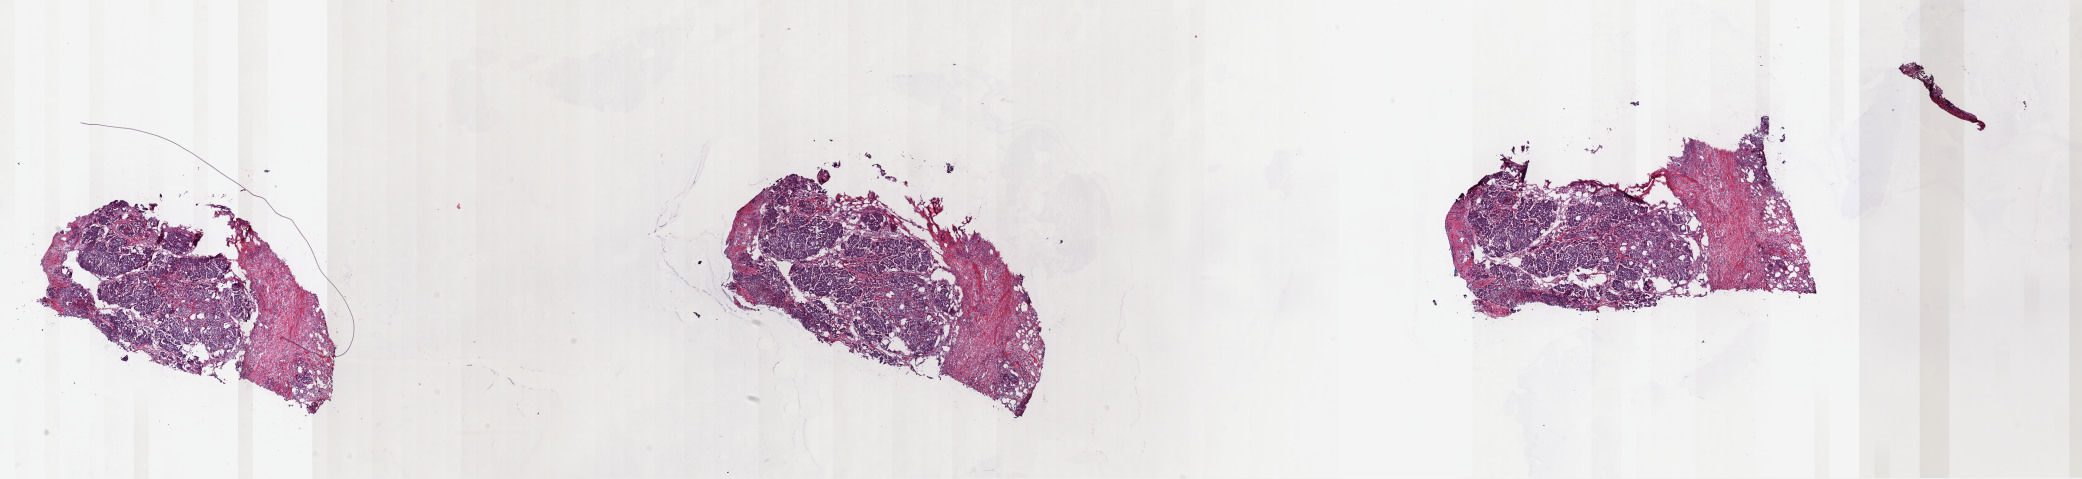
Digitized Hematoxylin and eosin (H&E) stained tissue section (whole slide) — shown as a low-resolution overview of the whole scanned area (about 32.9 x 7.6 mm, acquisition: 40x scan), frozen section from the top of the tissue portion, bladder, primary tumour sample. Male, age 65 years at initial diagnosis. Histologic grade: high grade. Composition of this section per pathologist review: tumour cells 55%, tumour nuclei 65%, normal cells 40%, stromal cells 0%, necrosis 5%. Inflammatory infiltration, as recorded: lymphocyte infiltration 10%, monocyte infiltration 1%, neutrophil infiltration 1%.
Diagnosis: Transitional cell carcinoma (posterior wall of bladder). AJCC pathologic stage: IV.